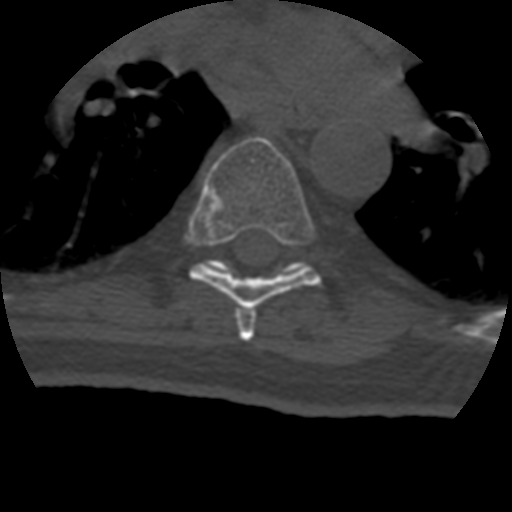
CT including the spine, one axial slice; slice 278 of 399 in the series (ordered by position); reconstruction kernel STANDARD; bone window (W 1800 / L 400 HU); 1.25 mm slice thickness; 512 × 512 image matrix. Patient age 69 years. From the clinical record (not read from this slice): primary cancer: prostate.
Annotated regions visible in this slice (semi-automatically segmented with operator editing):
- T6 vertebra: box from (x=235, y=309) to (x=256, y=341) px
- T7 vertebra: (x=189, y=137)–(x=321, y=309)
- T8 vertebra: (x=205, y=259)–(x=305, y=272)